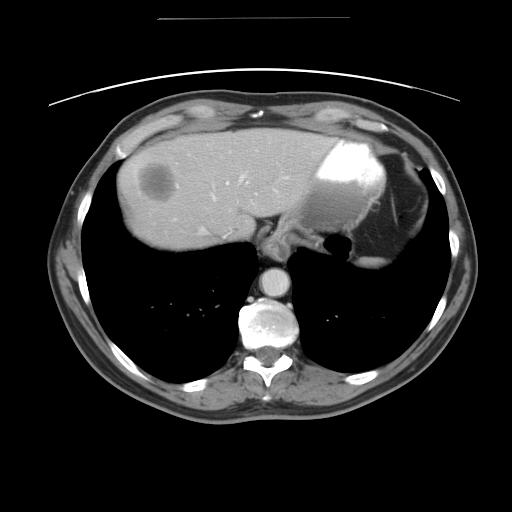
Contrast-enhanced abdominal CT, one axial slice; reconstruction kernel STANDARD; 120 kVp; intravenous contrast given; soft-tissue window (W 400 / L 40 HU); 5 mm slice thickness; 512 × 512 image matrix. Male patient, age 57 years. Case-level facts recorded for this patient, not image findings: diagnosis: colorectal cancer liver metastases, imaged before liver resection; multiple liver metastases: yes.
Structures marked on this image (outlined manually by an expert reader):
- hepatic veins: box from (x=199, y=174) to (x=242, y=235) px
- liver: (x=116, y=129)–(x=334, y=250)
- planned liver remnant (the part of the liver to remain after resection): (x=205, y=129)–(x=335, y=241)
- liver metastasis: (x=133, y=159)–(x=178, y=203)